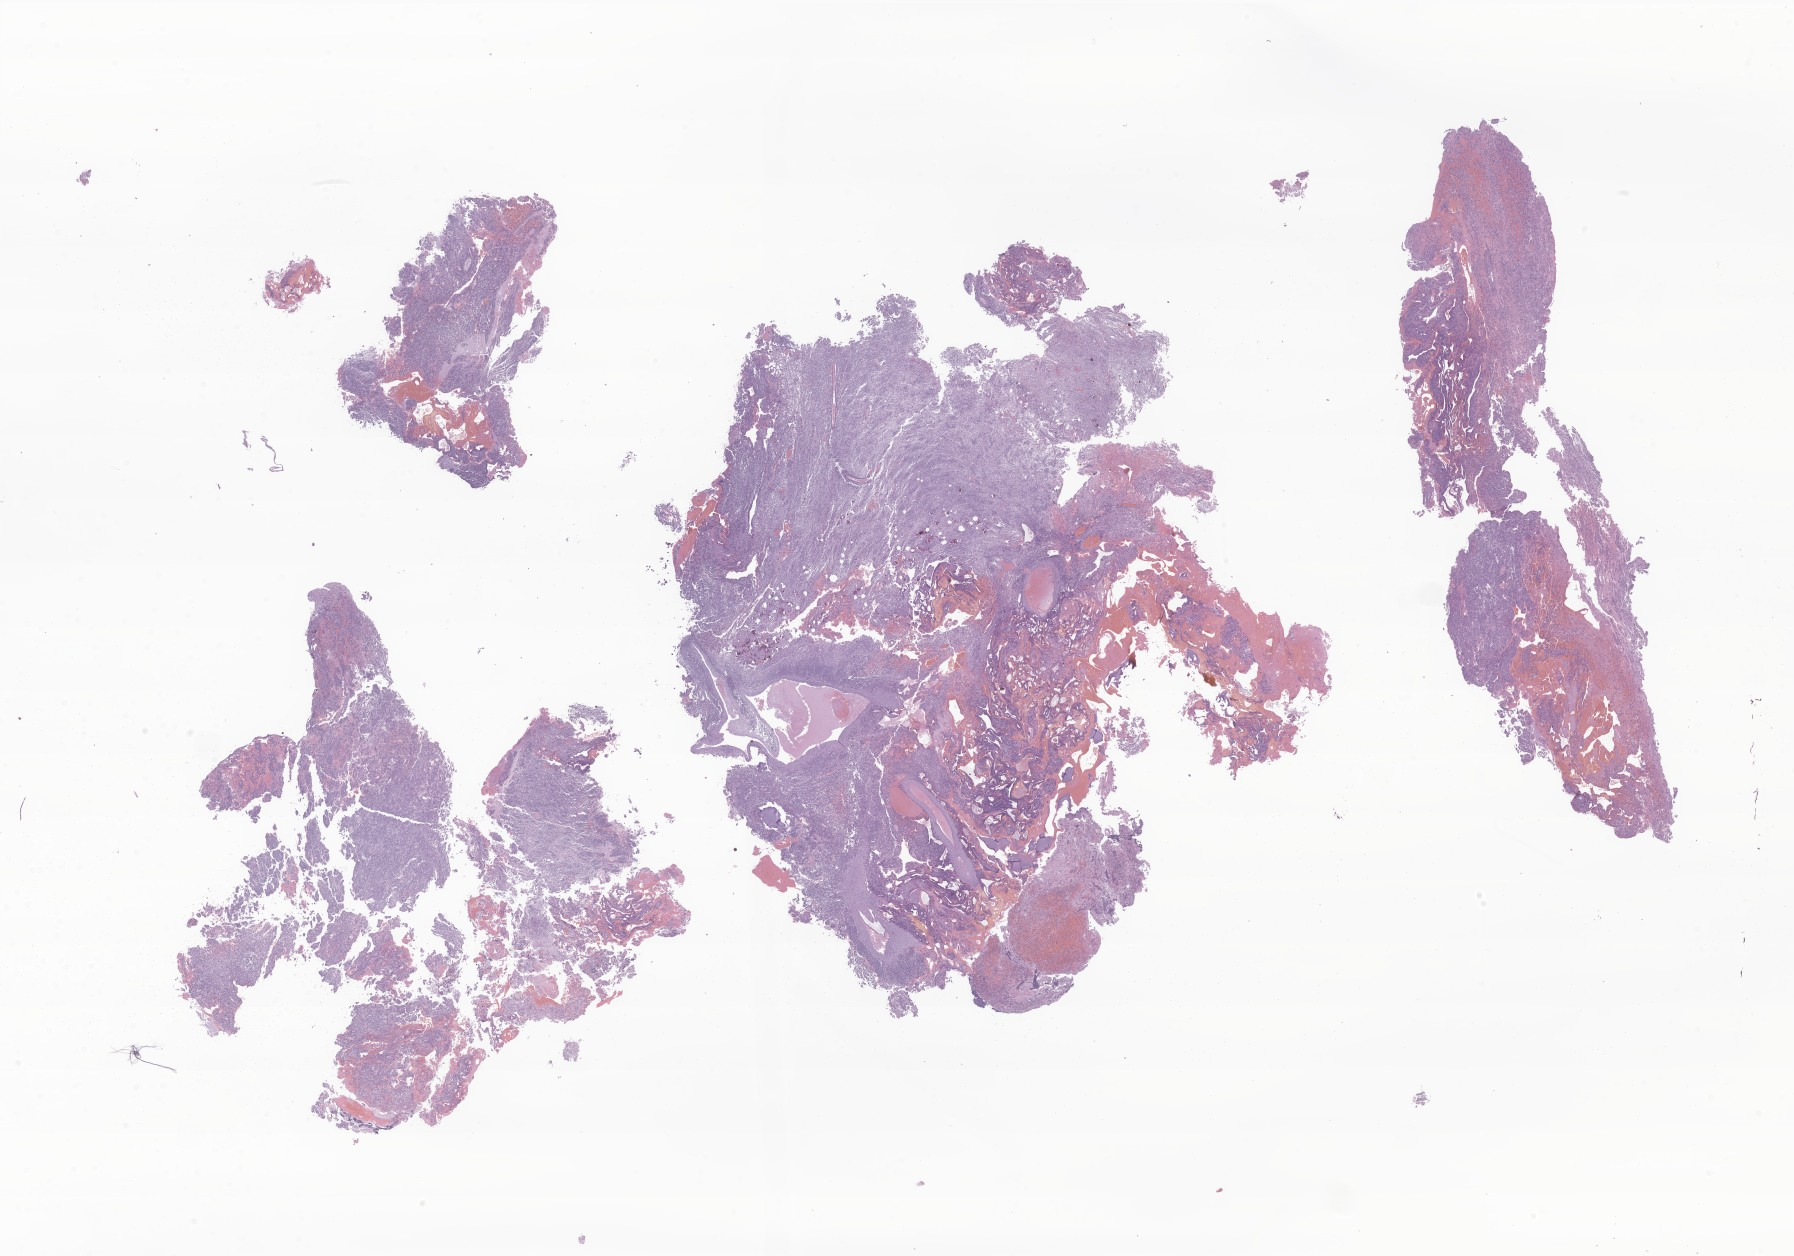
Whole-slide image, hematoxylin and eosin (H&E) stain of tumor tissue from the cerebellum, a low-resolution overview of the entire scanned area, about 30.3 x 21.2 mm. FFPE section. Patient: female, age 146 months.
Recorded diagnosis: Medulloblastoma, NOS.